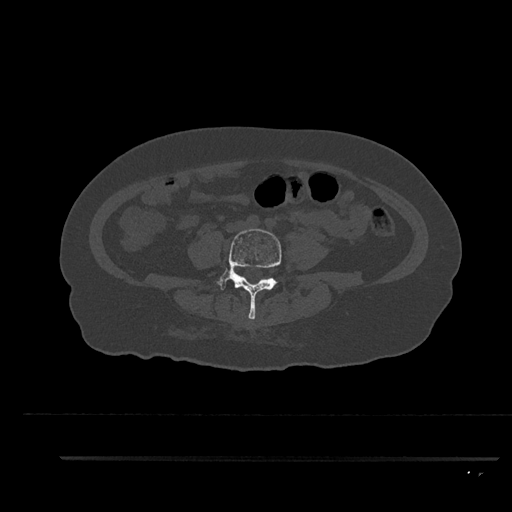
CT including the spine, one axial slice. Slice 16 of 797 in the series (ordered by position). Bone window (W 1800 / L 400 HU). 0.5 mm slice thickness. 512 × 512 image matrix. Patient: female, 44 years. Case-level facts recorded for this patient, not image findings: primary cancer: renal; vertebrae with lytic lesions (as recorded): L1.
Annotated regions visible in this slice (semi-automatic segmentation, software-assisted and operator-edited):
- L4 vertebra: bounding box <216,229,282,320> (left, top, right, bottom; pixels)